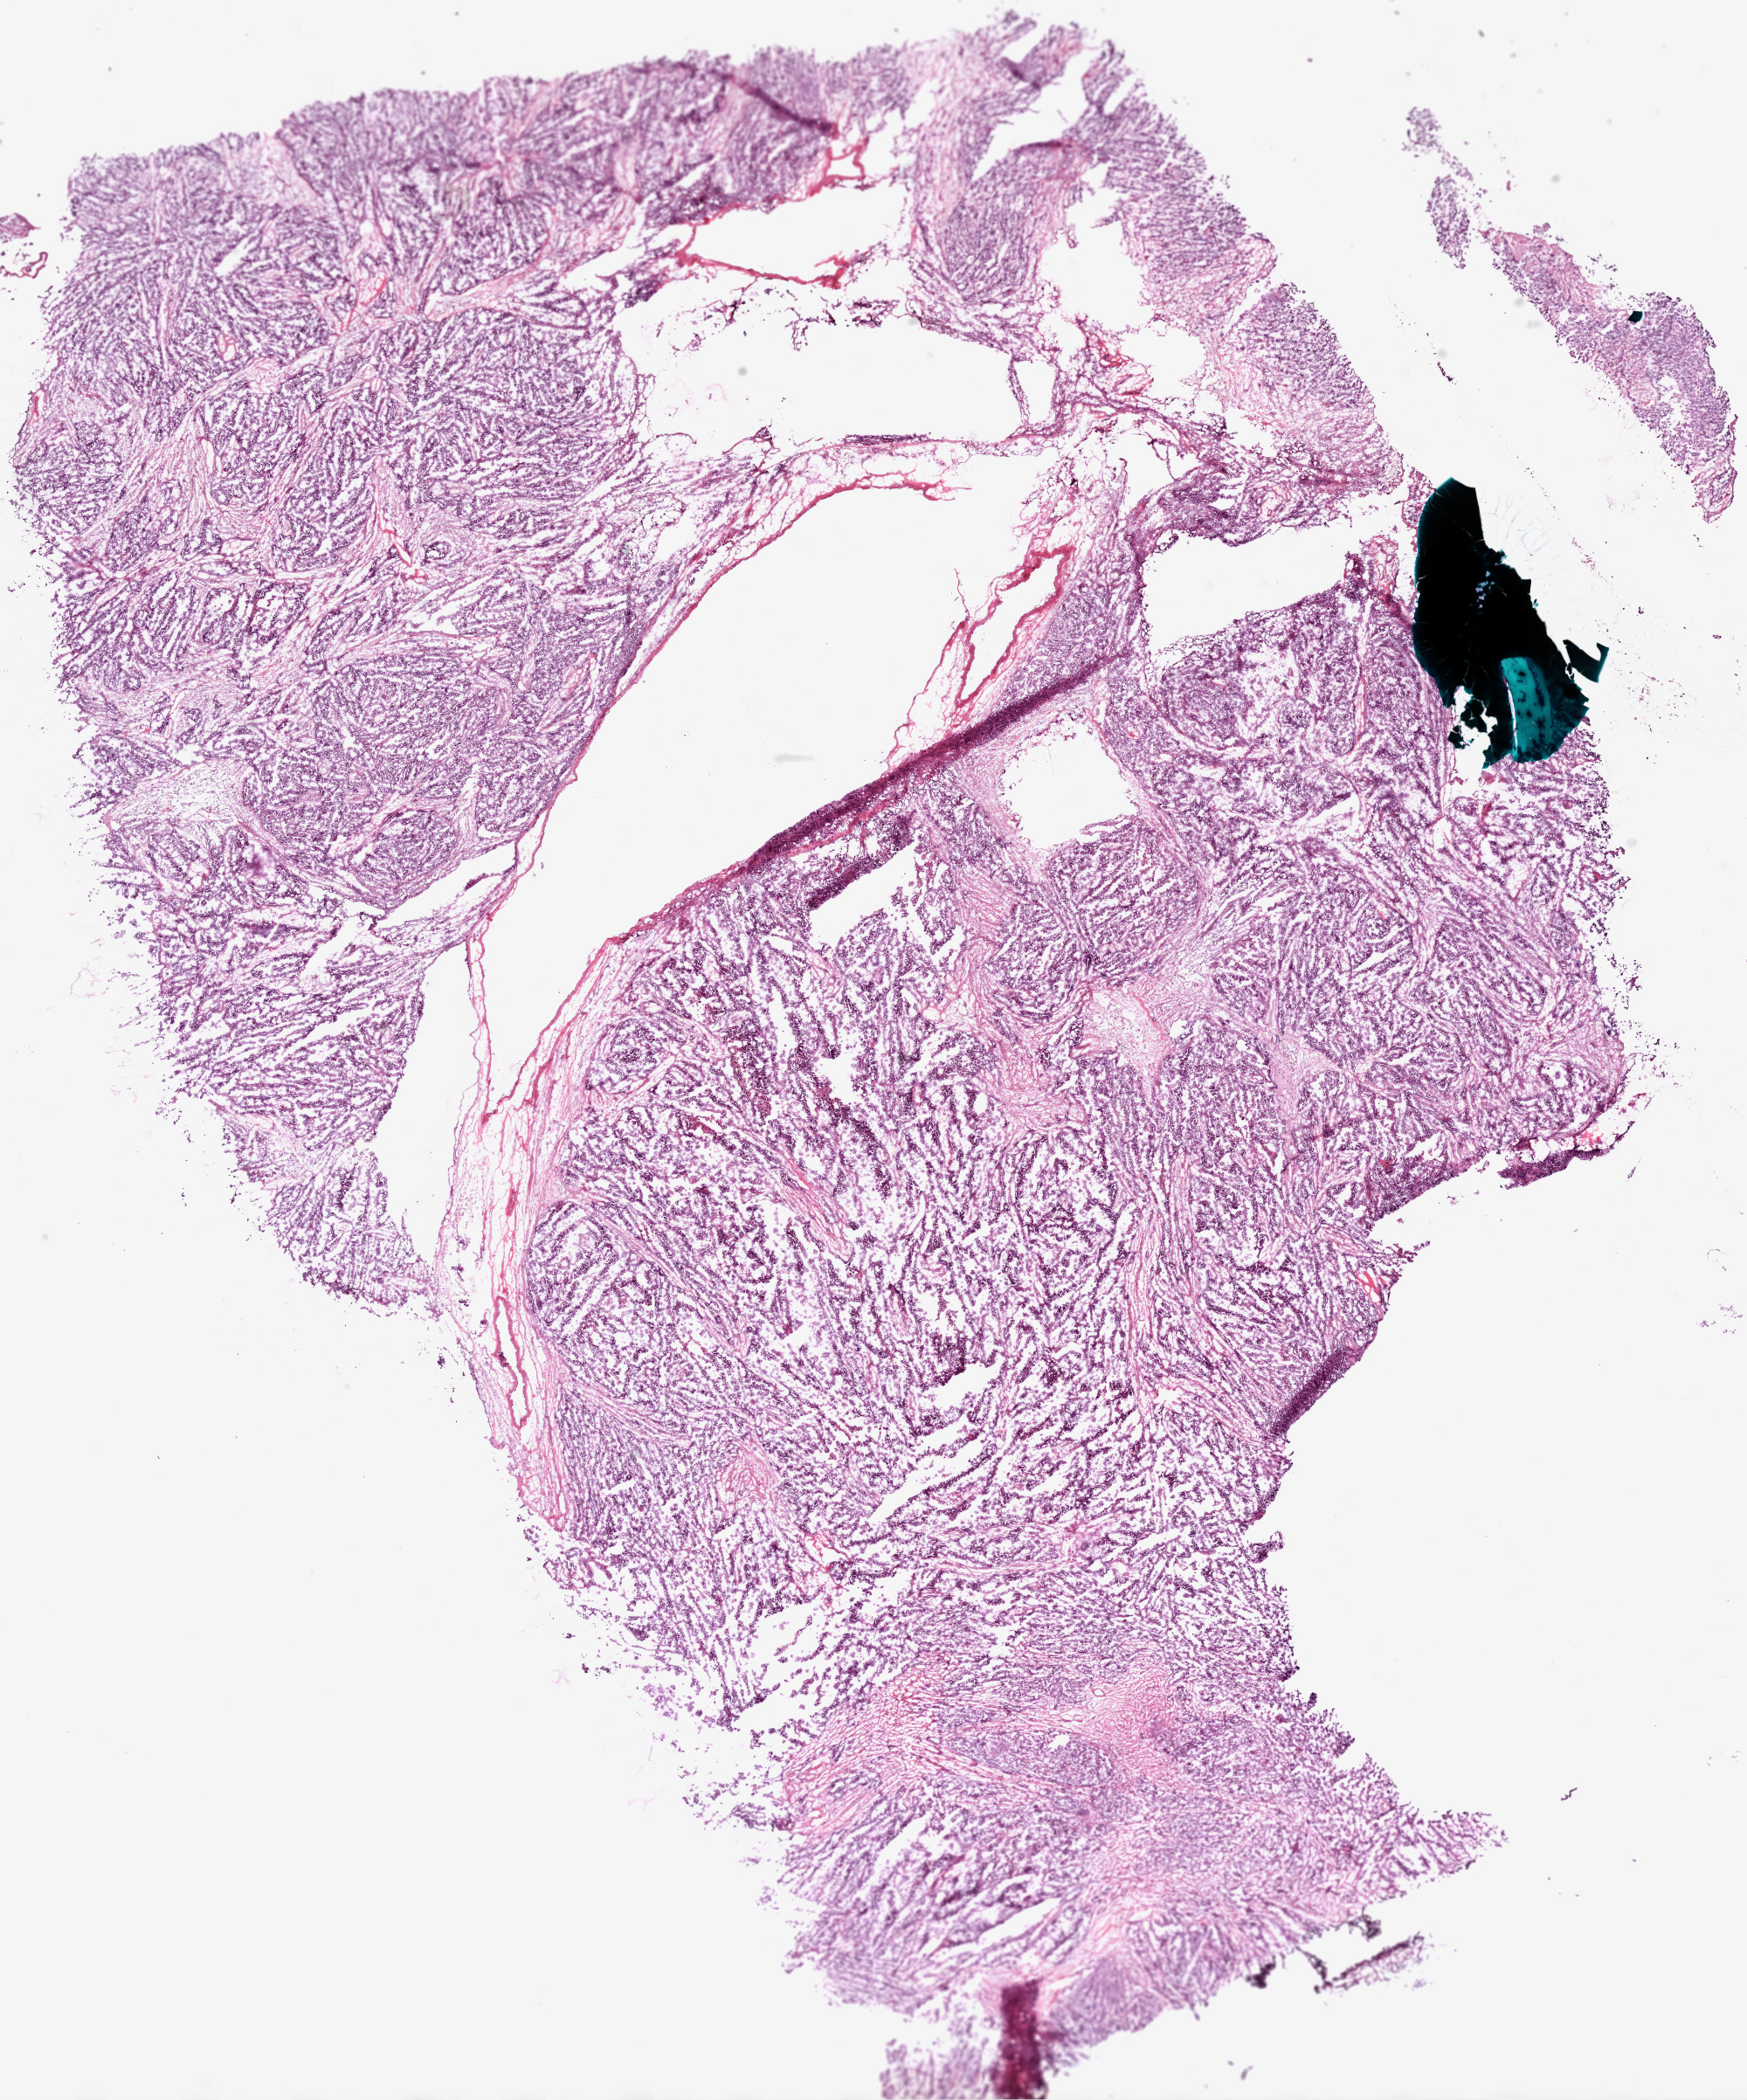
Digitized H&E tissue section (whole slide) — a low-resolution overview of the entire scanned area, about 16.0 x 19.3 mm. Frozen section. Sample: primary tumour, ovary. Female patient; age at initial diagnosis 57 years. Histologic grade: GX (grade cannot be assessed). Pathologist review of this section (percent, as recorded): tumour cells 94%, tumour nuclei 95%, normal cells 0%, stromal cells 5%, necrosis 1%.
FIGO stage: IV. Pathologic diagnosis: Serous cystadenocarcinoma, NOS.